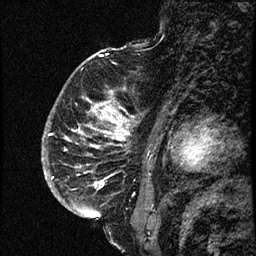
Breast MRI (dynamic contrast-enhanced), one sagittal slice. Slice 48 of 66 in the series (ordered by position). Dynamic contrast-enhanced study with each time point stored as its own series, time point 2 of 3 at this slice position (early post-contrast, ordered by acquisition time). 1.5 T. TE 4.2 ms, TR 17.6 ms. 256 × 256 image matrix. Female patient. Case-level facts recorded for this patient, not image findings: setting: breast cancer imaged before/during neoadjuvant chemotherapy; receptor status: HER2-positive.
Annotated regions visible in this slice (semi-automatic segmentation, software-assisted and operator-edited):
- analysis volume of interest (the breast-tissue region the enhancement analysis was run in; not a lesion): bounding box <52,69,140,209> (left, top, right, bottom; pixels)
- tumour enhancement mask (voxels above the 100 % enhancement threshold inside the analysis volume of interest): <52,92,135,207>